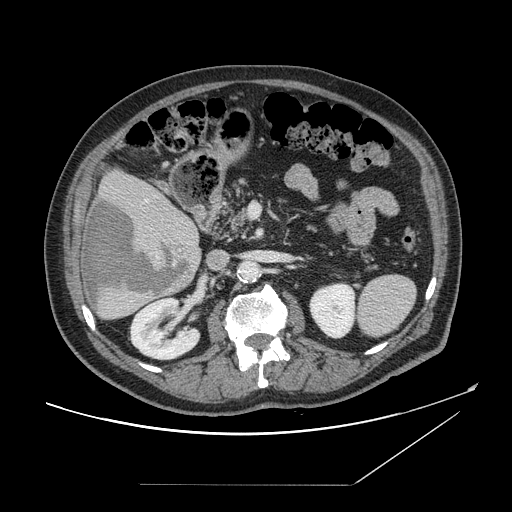
Contrast-enhanced abdominal CT, one axial slice. Position 73 of 166 along the scan axis. Intravenous contrast given. Soft-tissue window (W 400 / L 40 HU). 2.5 mm slice thickness. 512 × 512 image matrix, field of view 416 × 416 mm. Male patient, age 80 years. Case-level facts recorded for this patient, not image findings: diagnosis: colorectal cancer liver metastases, imaged before liver resection; multiple liver metastases: no; largest metastasis: 2.2 cm; chemotherapy before resection: no.
Outlined on this slice (manually delineated by an expert):
- hepatic veins: bounding box <146,200,149,203> (left, top, right, bottom; pixels)
- liver: <81,168,201,320>
- planned liver remnant (the part of the liver to remain after resection): <104,167,190,223>
- liver metastasis: <84,199,190,308>